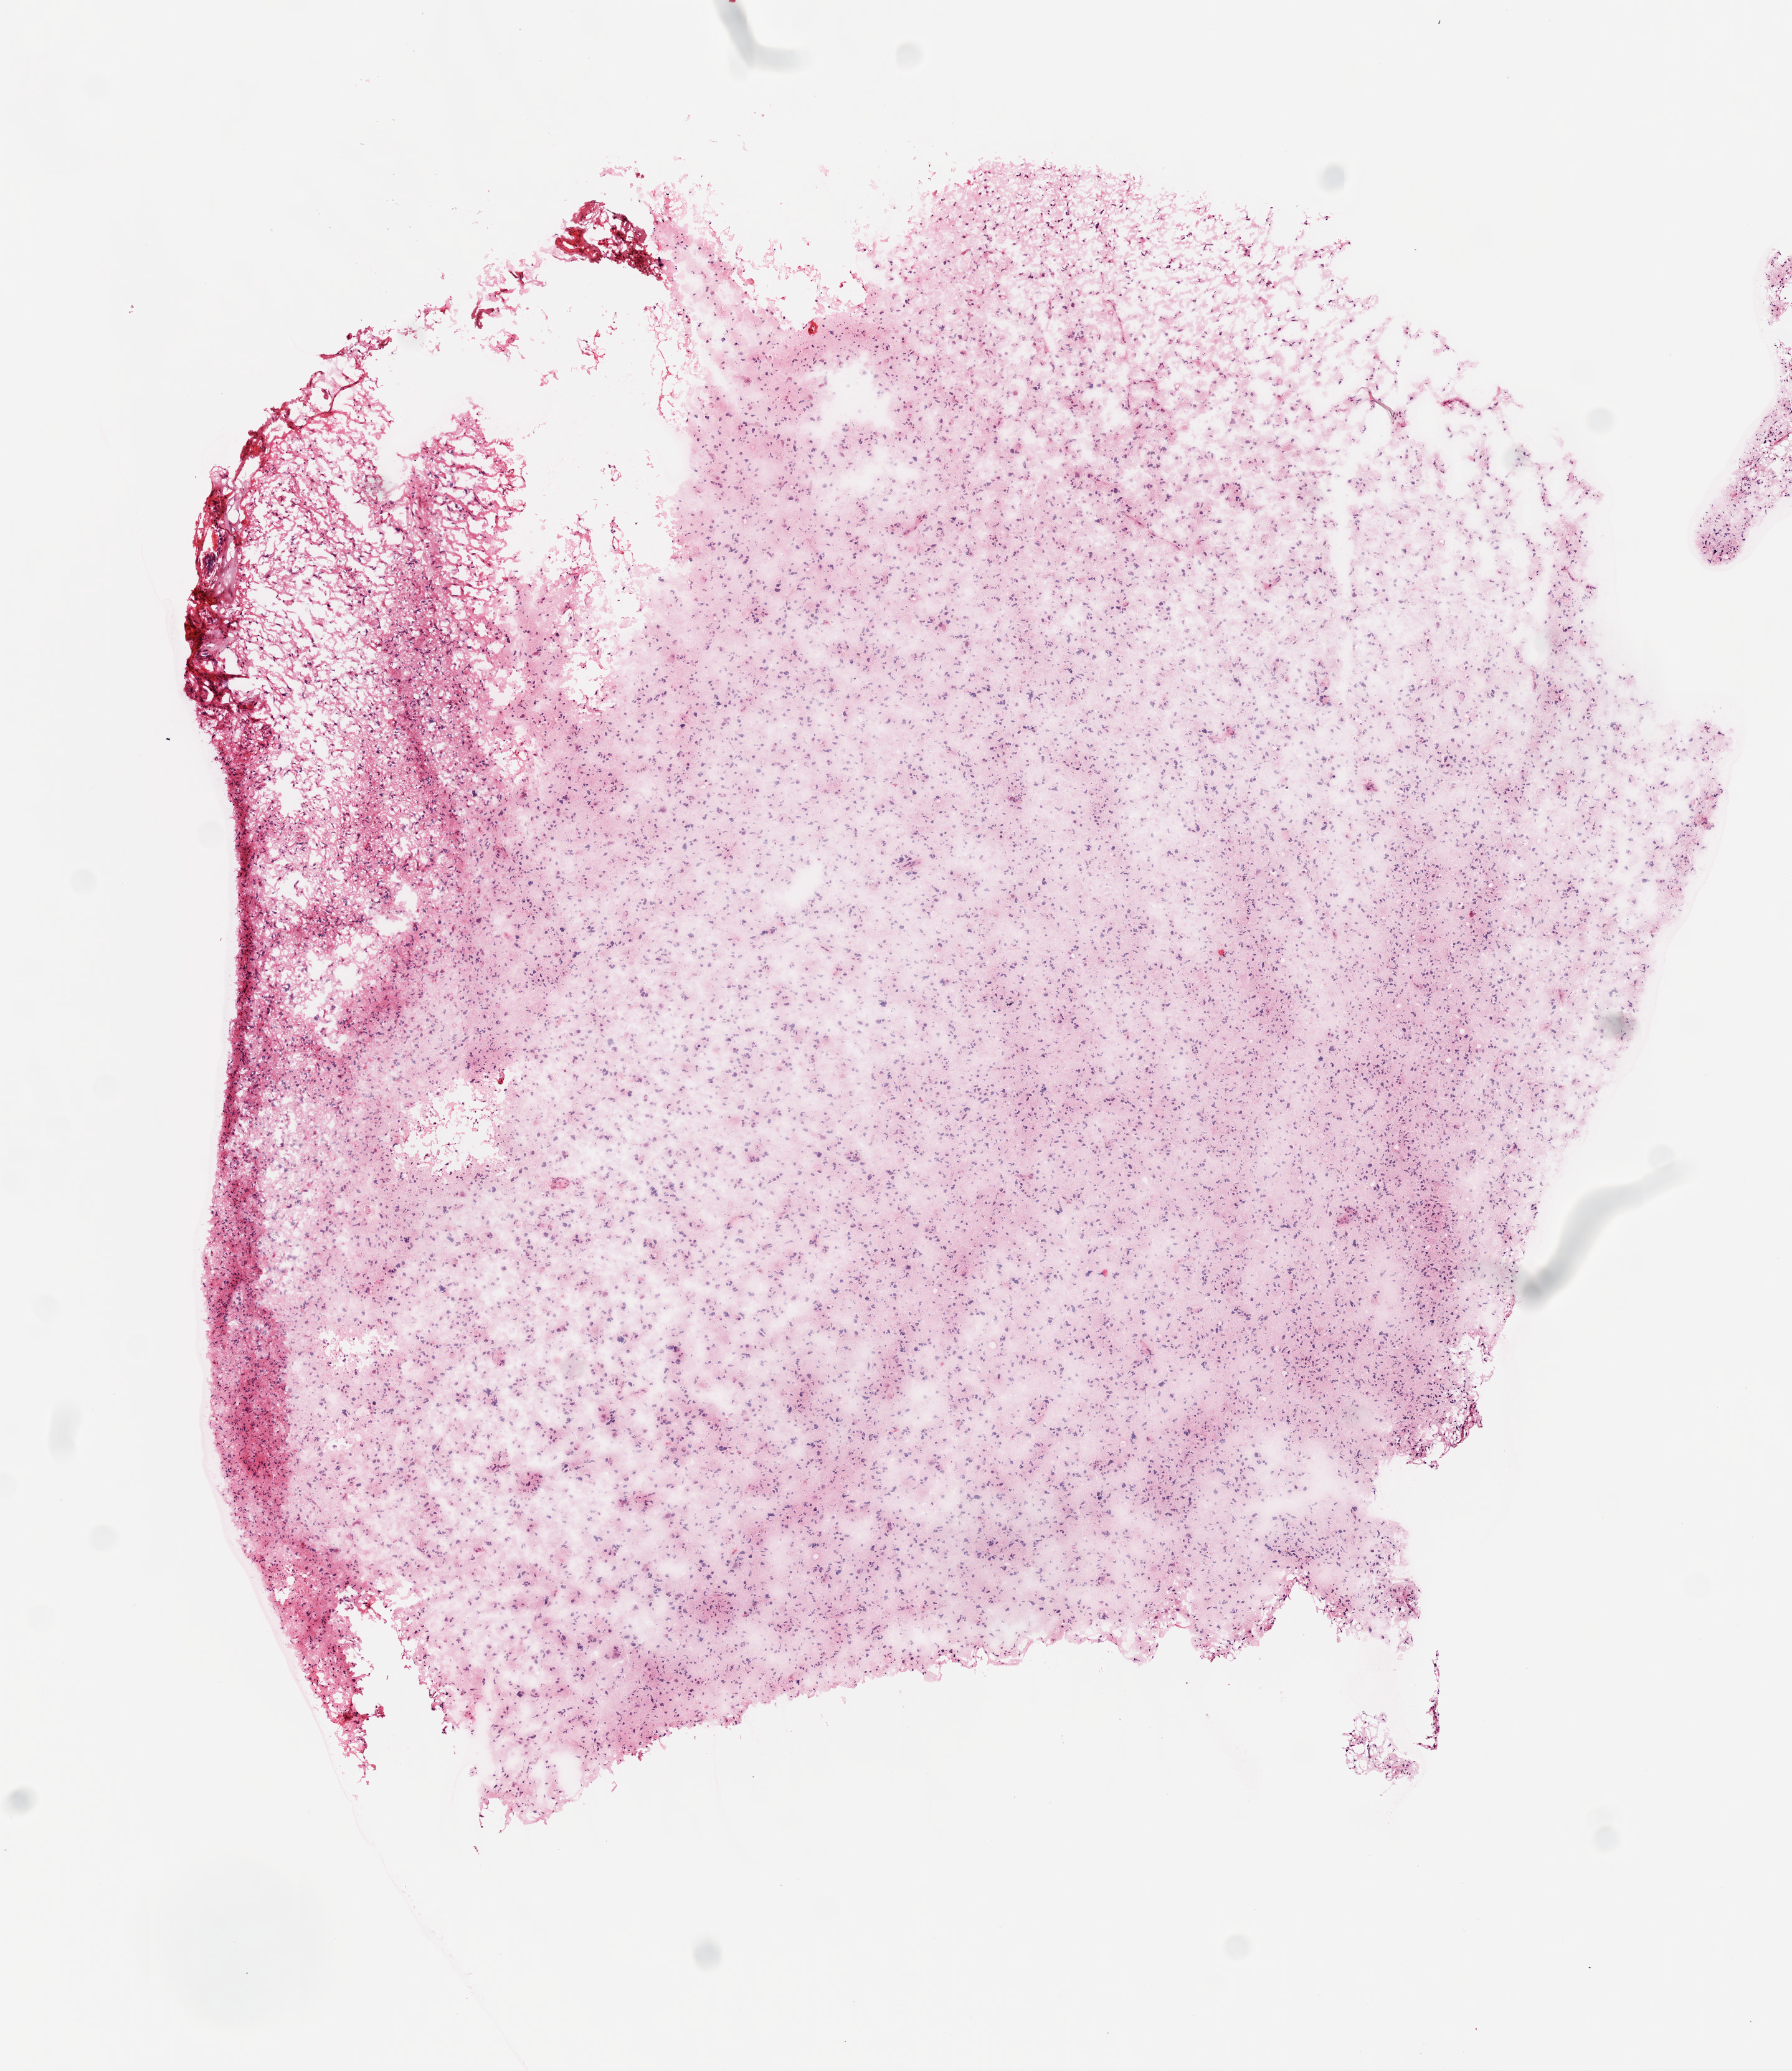
Digitized H&E tissue section (whole slide) — whole scanned area (about 5.8 x 6.7 mm) shown as a low-resolution overview. Frozen section from the bottom of the tissue portion. Brain, primary tumour sample. Male patient; age at initial diagnosis 40 years. Pathologist review of this section (percent, as recorded): tumour cells 85%, tumour nuclei 85%, normal cells 0%, stromal cells 10%, necrosis 5%.
* diagnosis: Glioblastoma